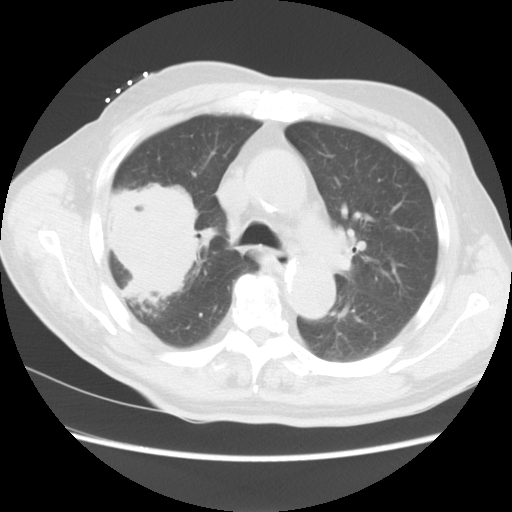
Chest CT, one axial slice. Slice 10 of 15 in the series (ordered by position). Reconstruction kernel STANDARD. Lung window (W 1500 / L -600 HU). 512 × 512 image matrix. Patient: male, 68 years. Case-level facts recorded for this patient, not image findings: clinical TNM (as recorded): T4 N3 M0.
Structures marked on this image (bounding box drawn by a radiologist):
- lung tumour (recorded histology: squamous cell carcinoma): box from (x=97, y=178) to (x=206, y=324) px